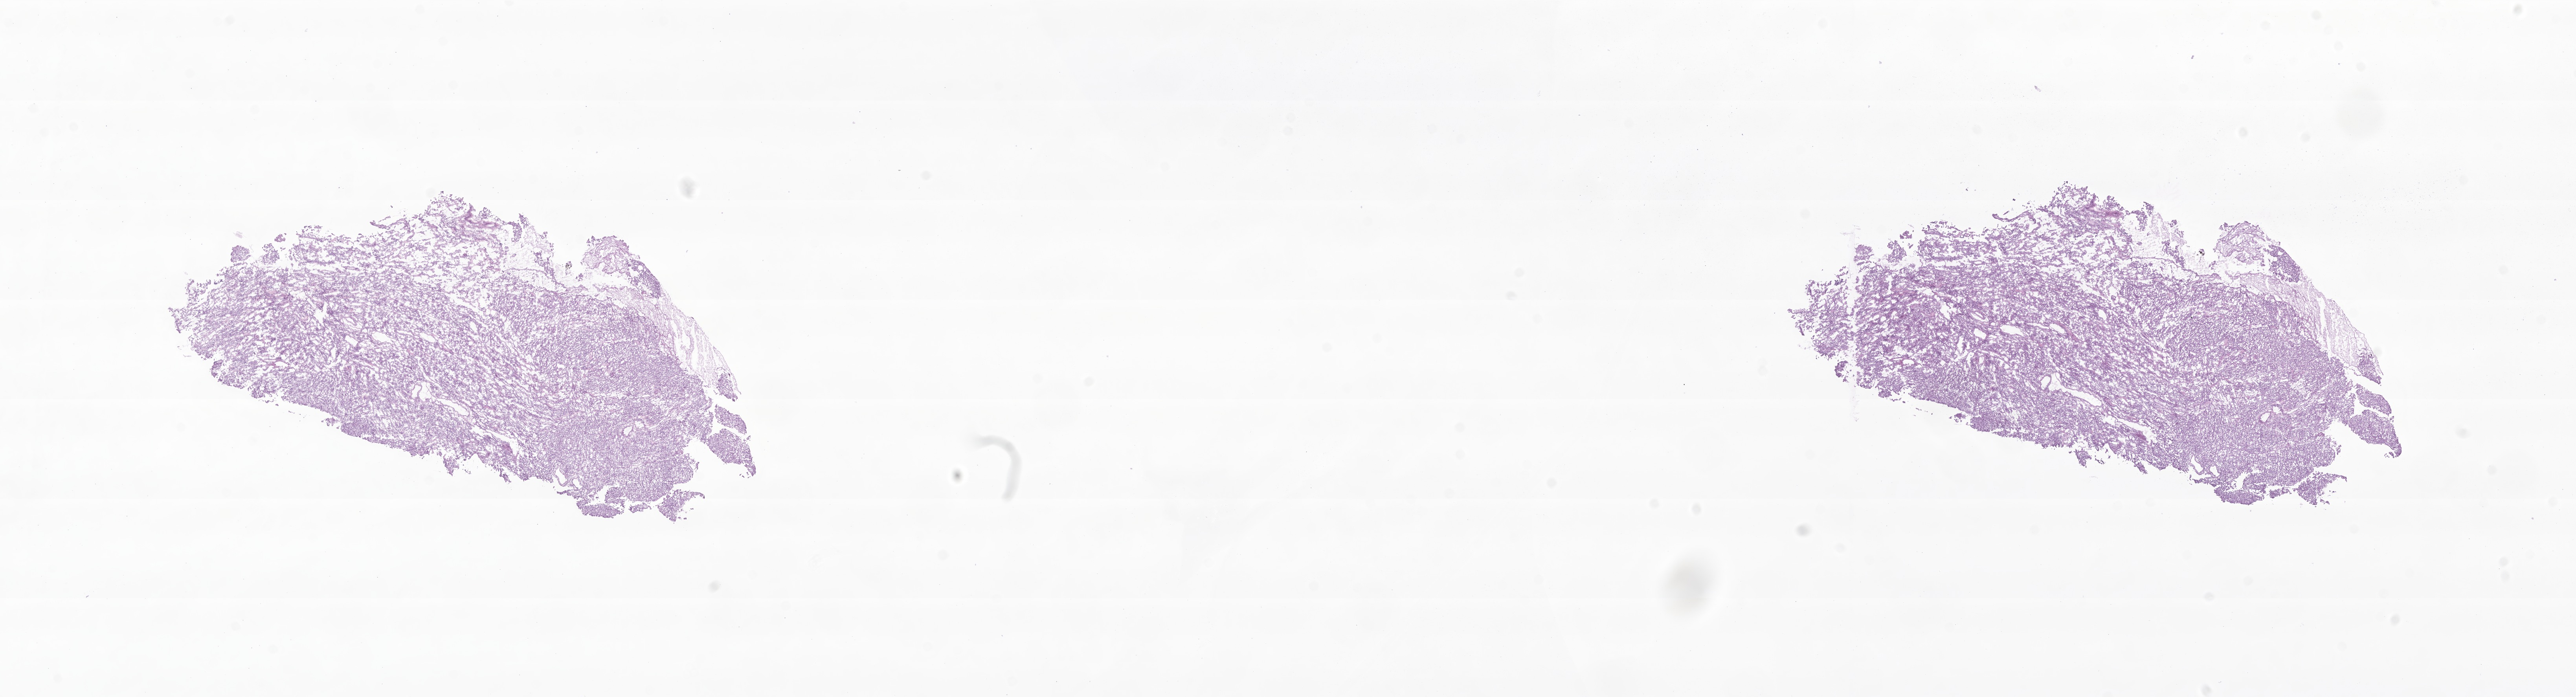
Digitized H&E-stained section of tumor tissue from the meninges — shown as a low-resolution overview of the whole scanned area (about 27.6 x 7.5 mm), frozen section (OCT-embedded). Patient male; age 130 months.
* recorded diagnosis: Meningioma, NOS